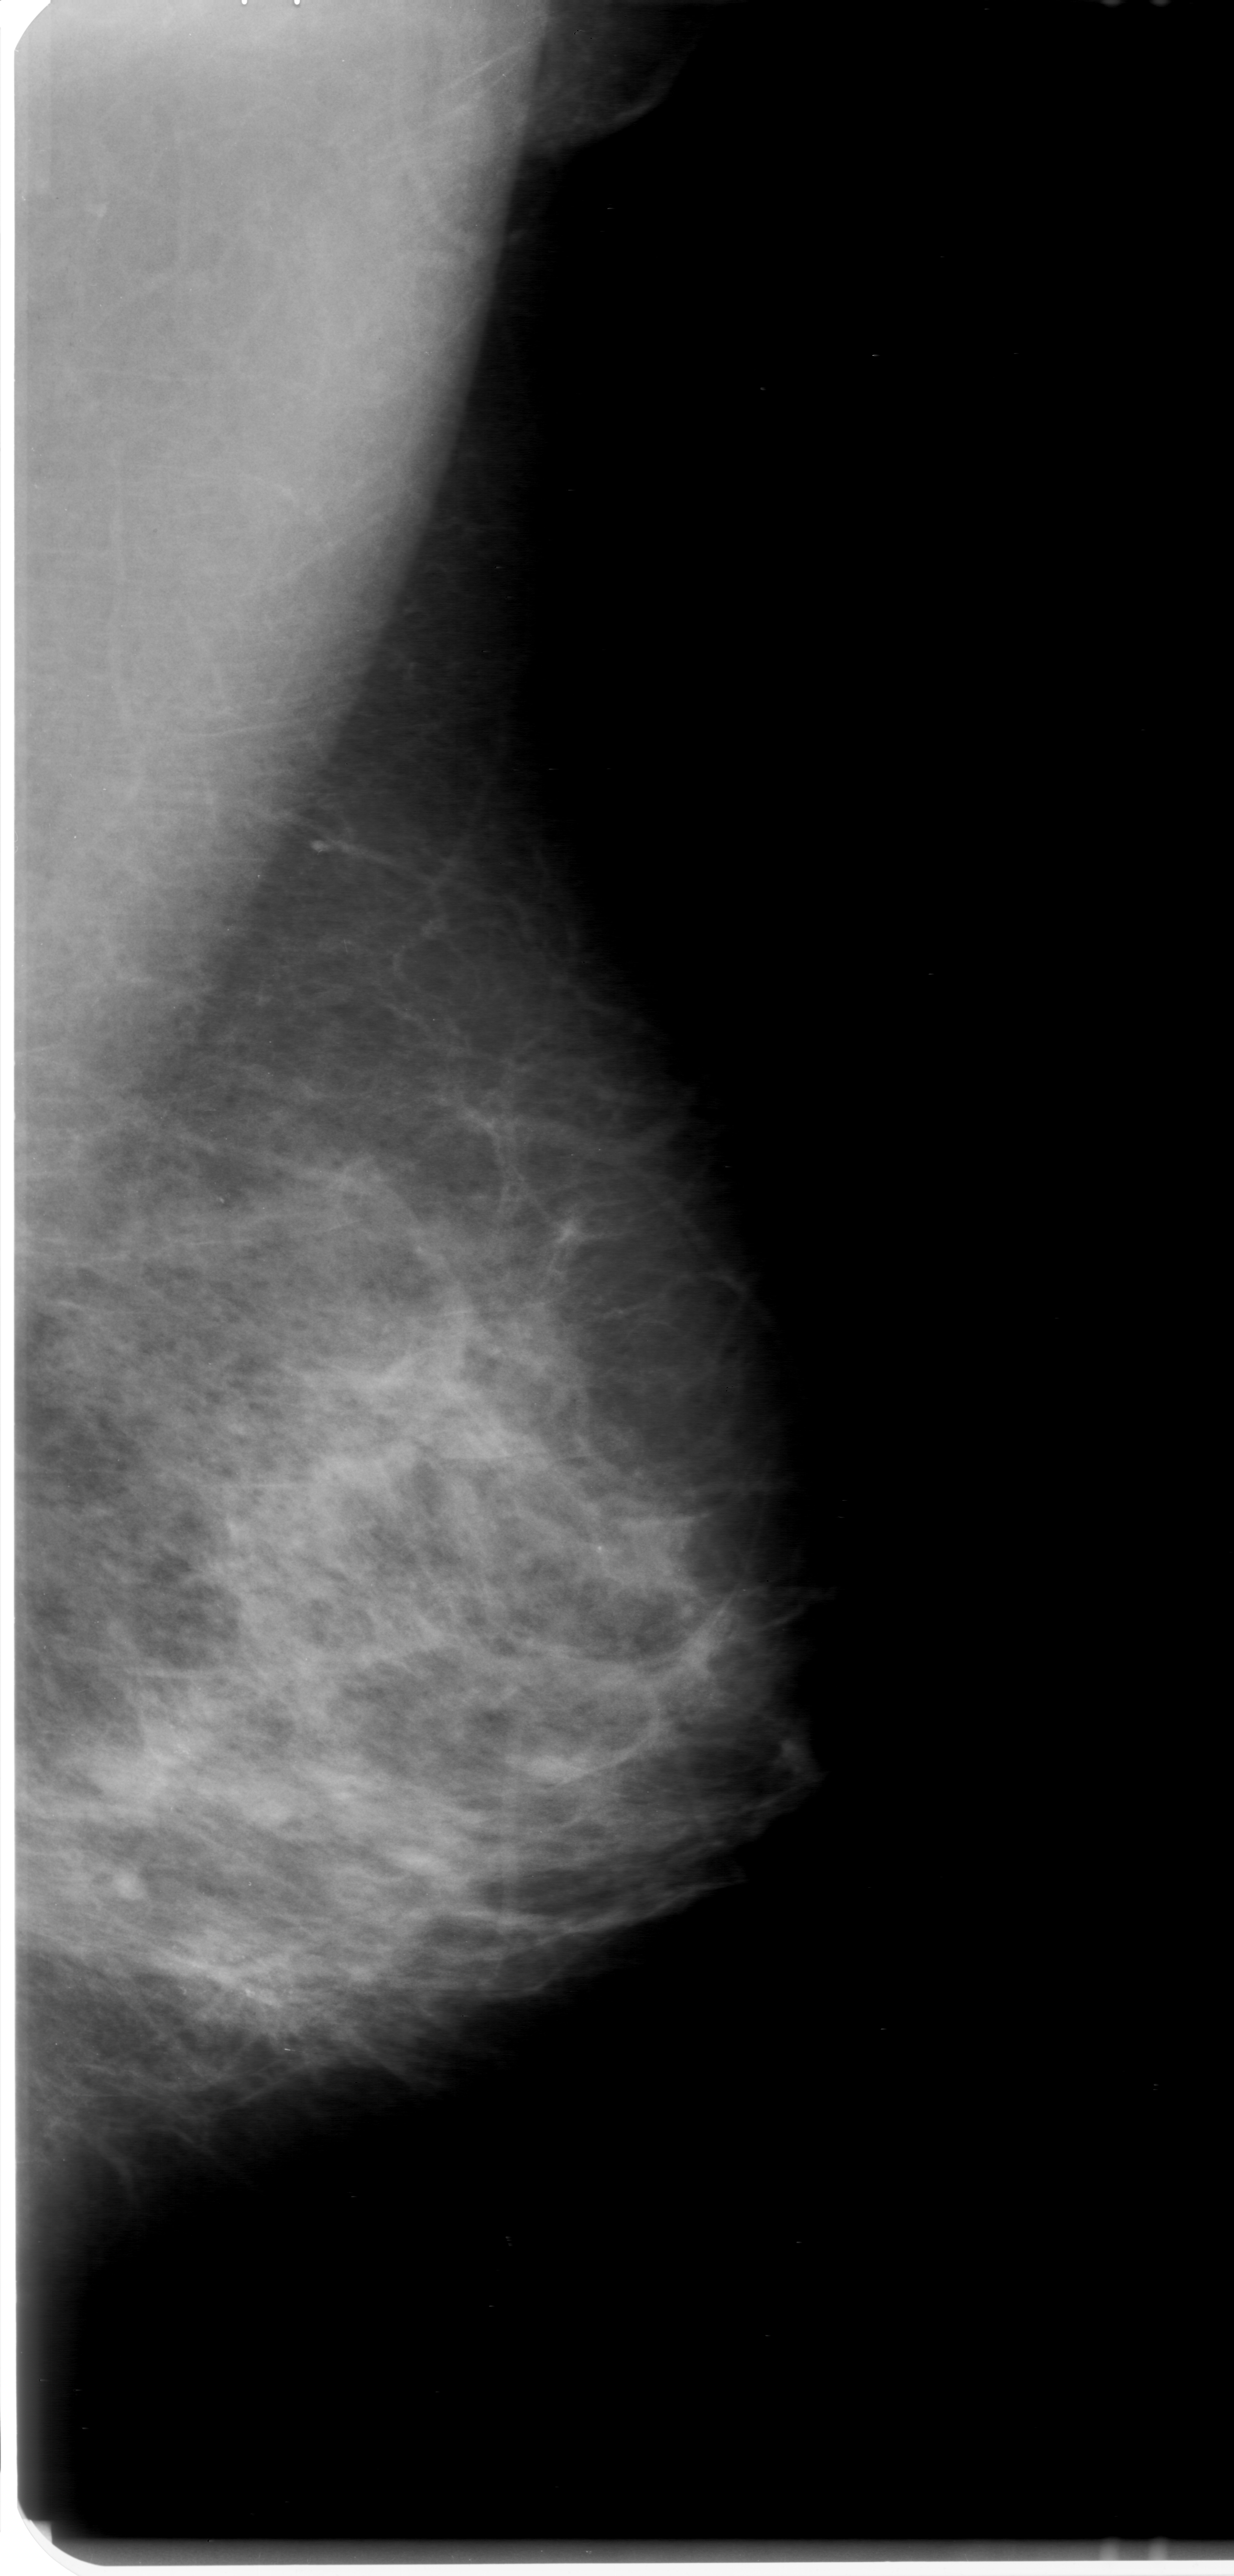
Mammogram (digitized film). Left breast. MLO view. 1234 × 2576 image matrix.
Marked abnormalities (boxes around the expert regions of interest):
- calcifications, morphology pleomorphic, distribution clustered; BI-RADS assessment category 0 (incomplete: needs additional imaging); pathology result (as recorded, not read from the image): malignant: bounding box <64,1623,325,2133> (left, top, right, bottom; pixels)